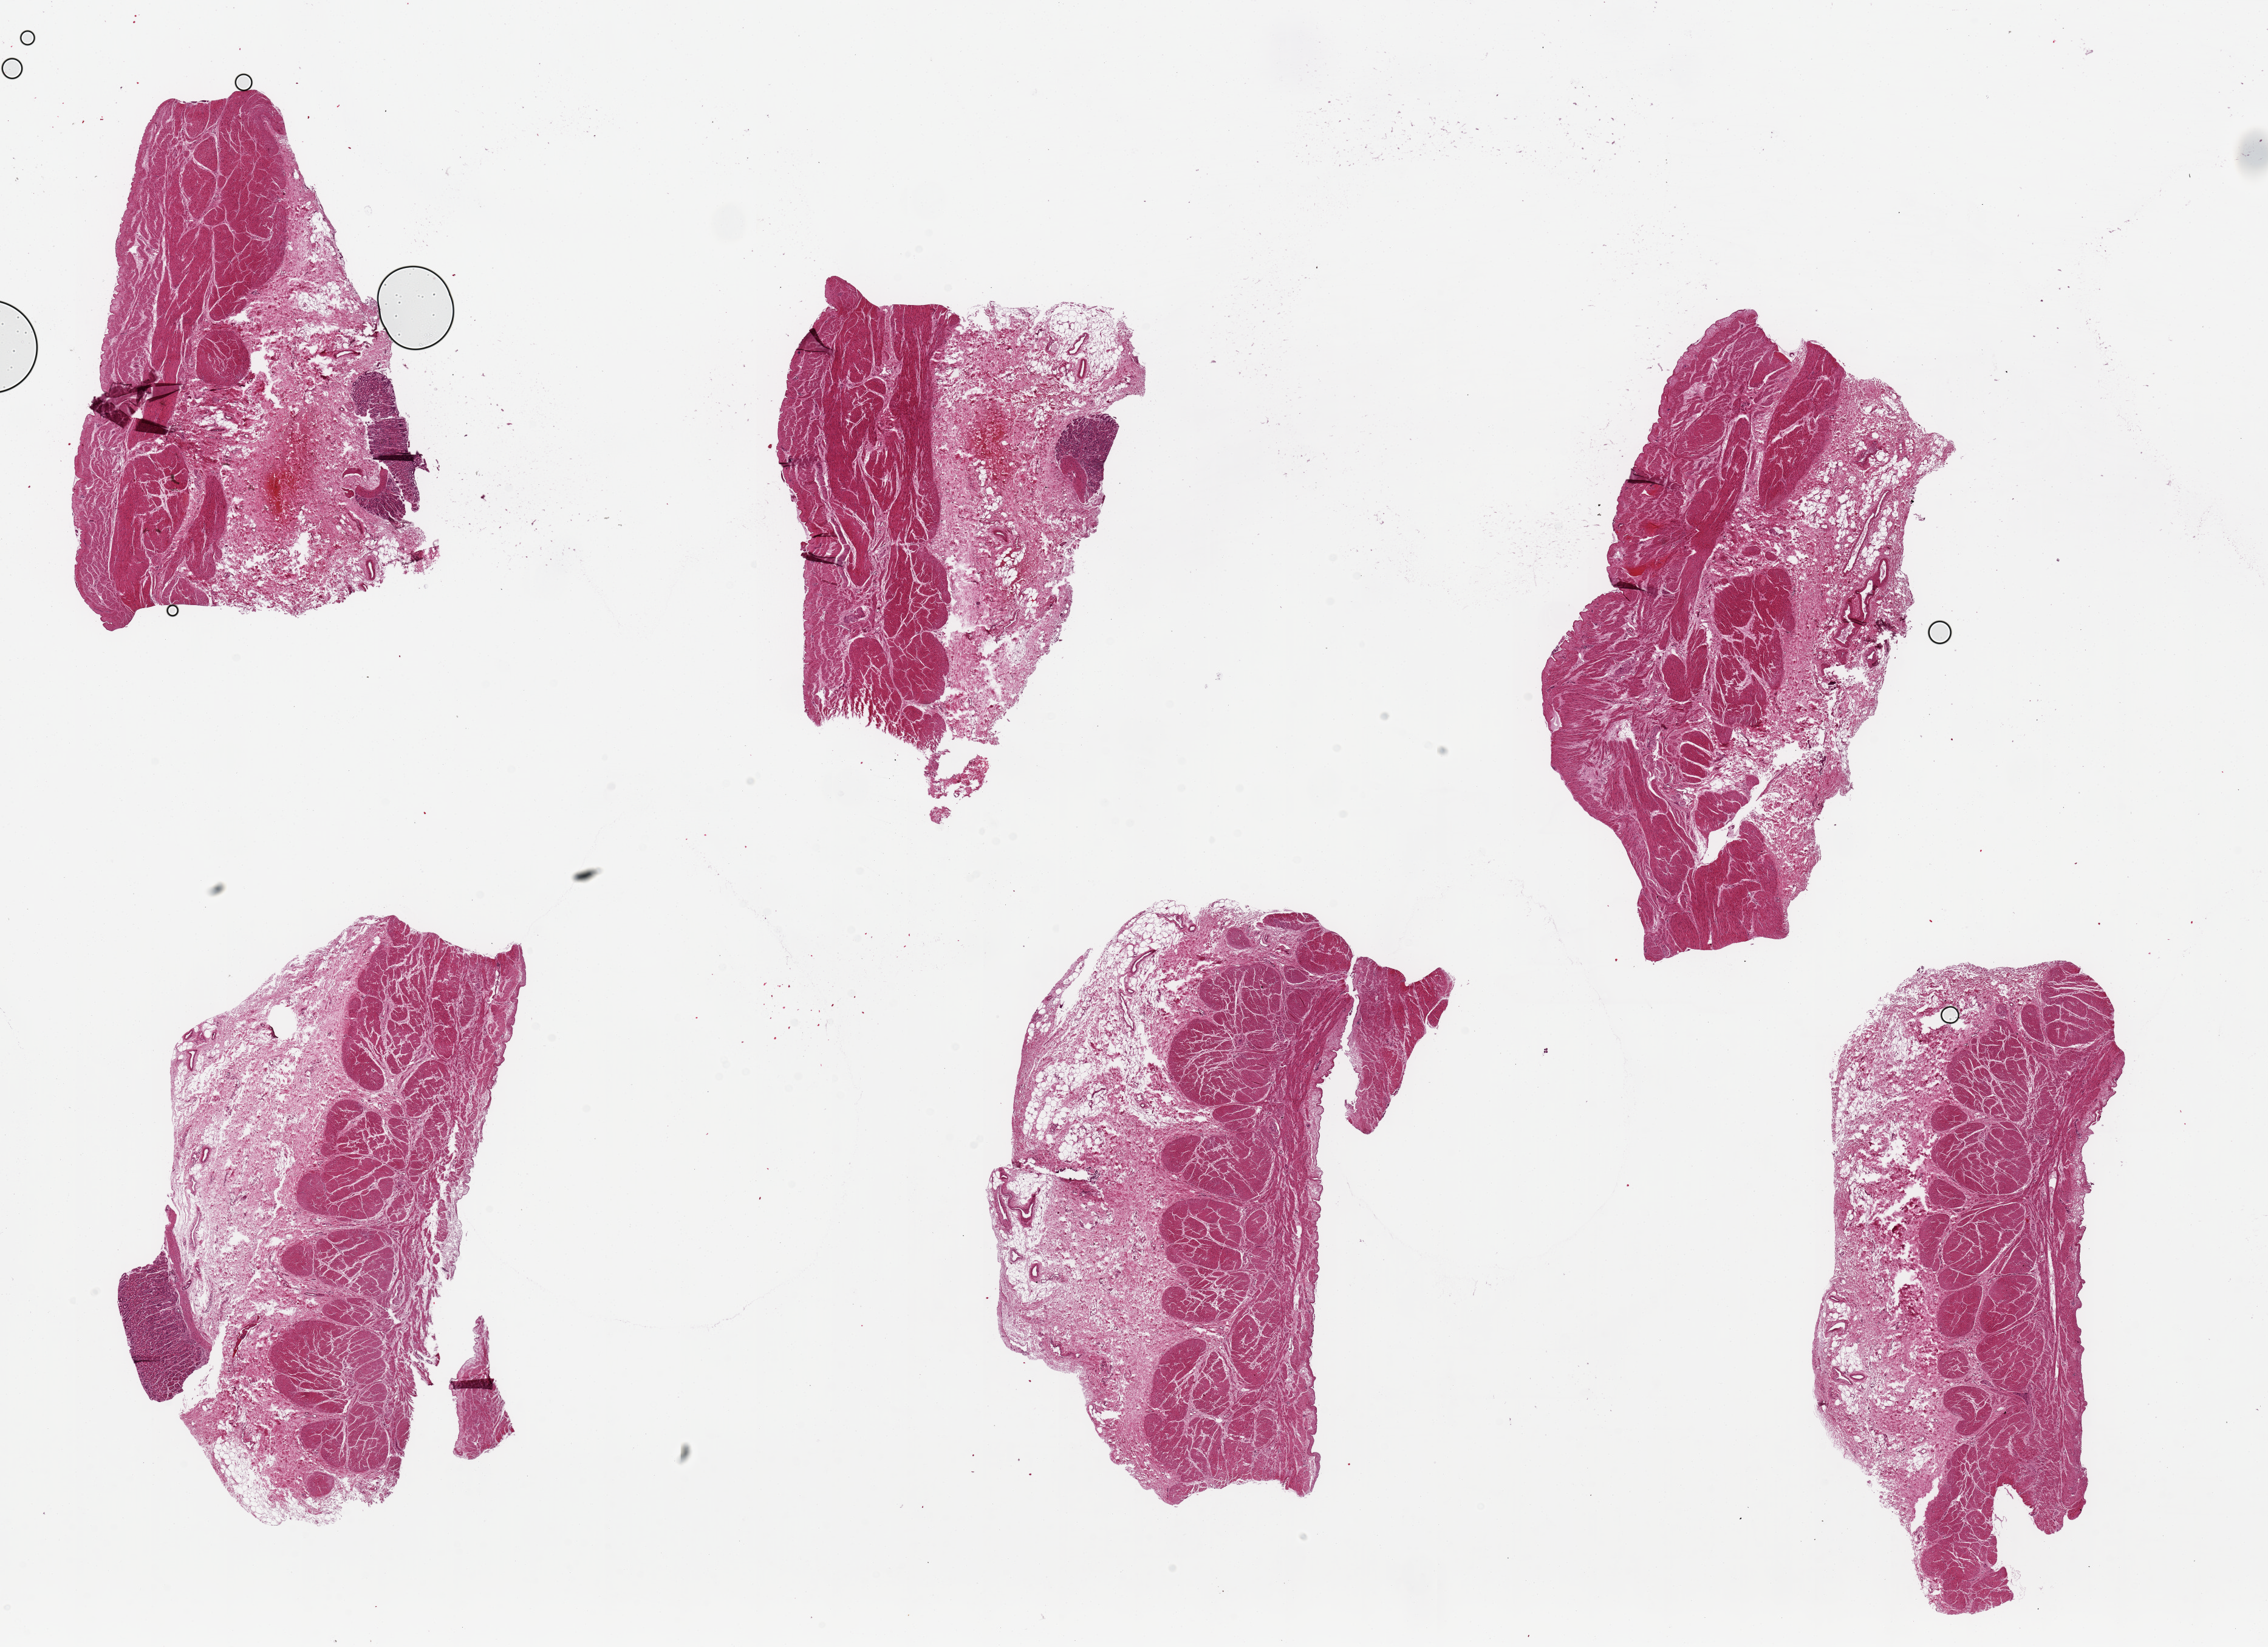
Digitized haematoxylin and eosin-stained section — low-resolution overview of the scanned area, about 29.5 x 21.4 mm (from a 20x scan). PAXgene-fixed paraffin-embedded (PFPE) section. Section of stomach (target tissue). Donor tissue sample.
* reviewer comment on this tissue sample: 6 pieces ~5x5mm, mainly muscularis, mucosa sloughed, focally present, where present, well-preserved